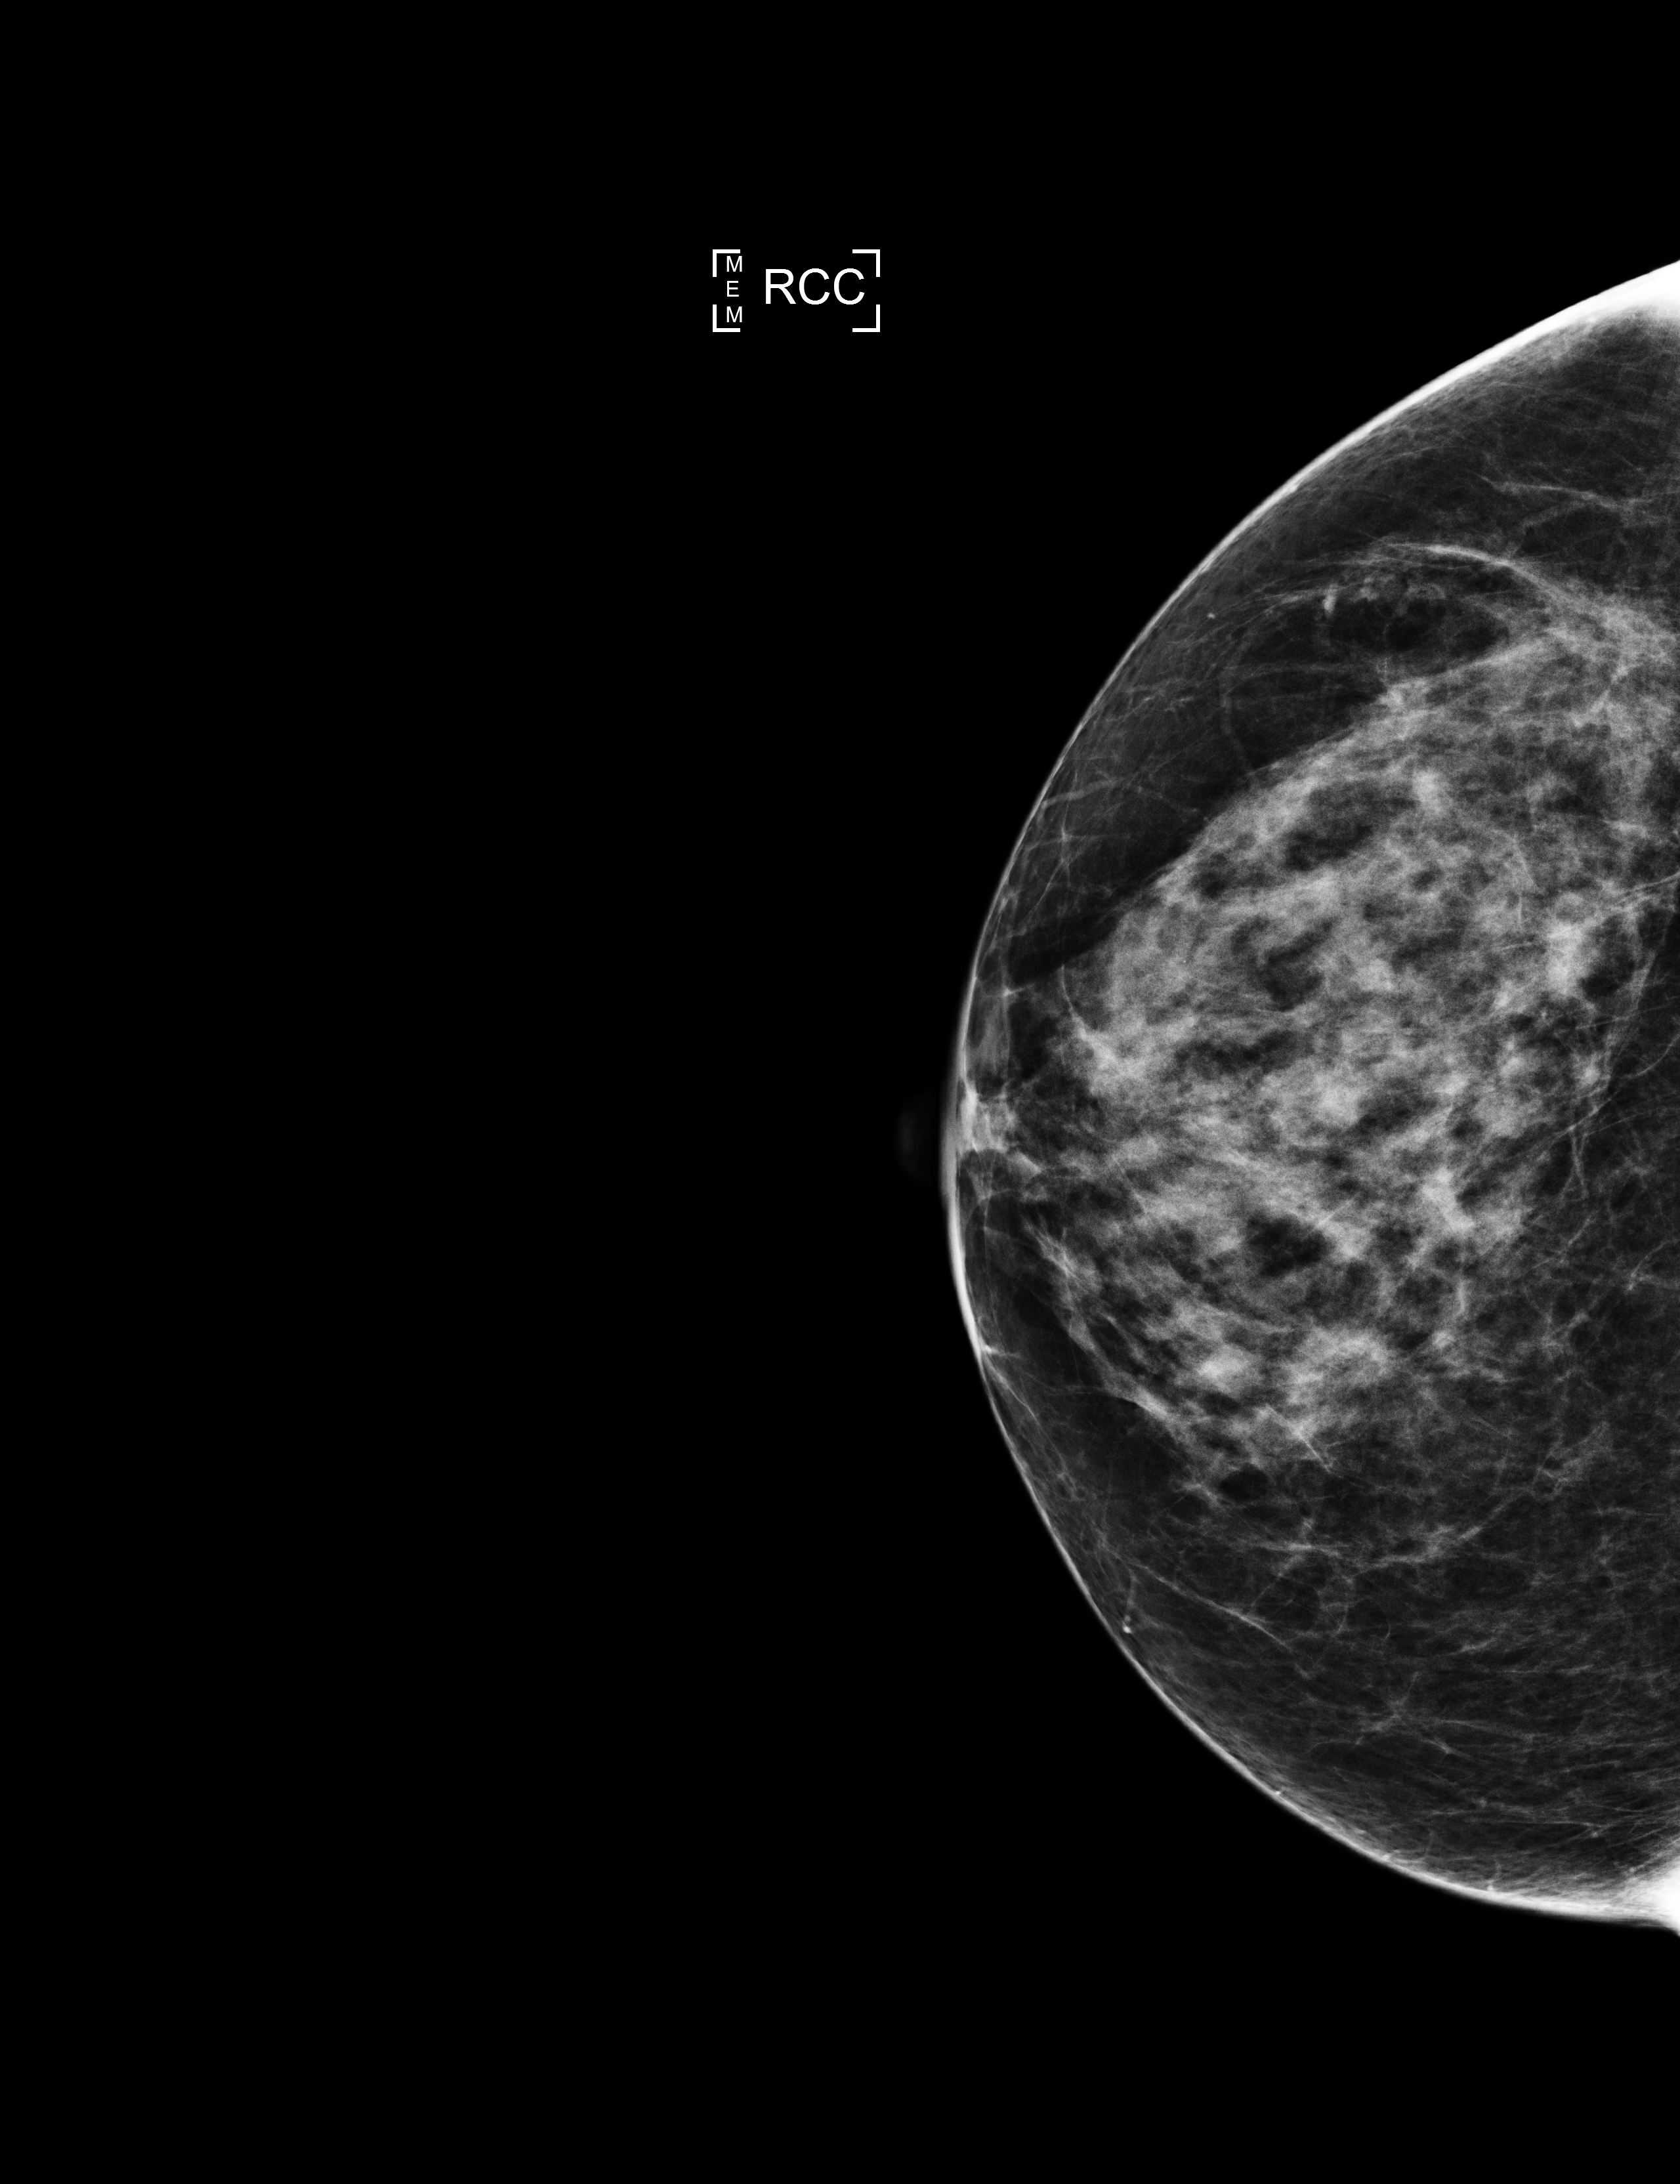
Full-field digital mammogram (FFDM), right breast, CC view, screening examination, compressed breast thickness 57 mm. Female patient, age 57 years.
Breast density at the screening exam (both breasts): heterogeneously dense (BI-RADS density category c). Final BI-RADS category for the screening round (tomosynthesis exam, both breasts): category 1. Recall: no recall after this screen.